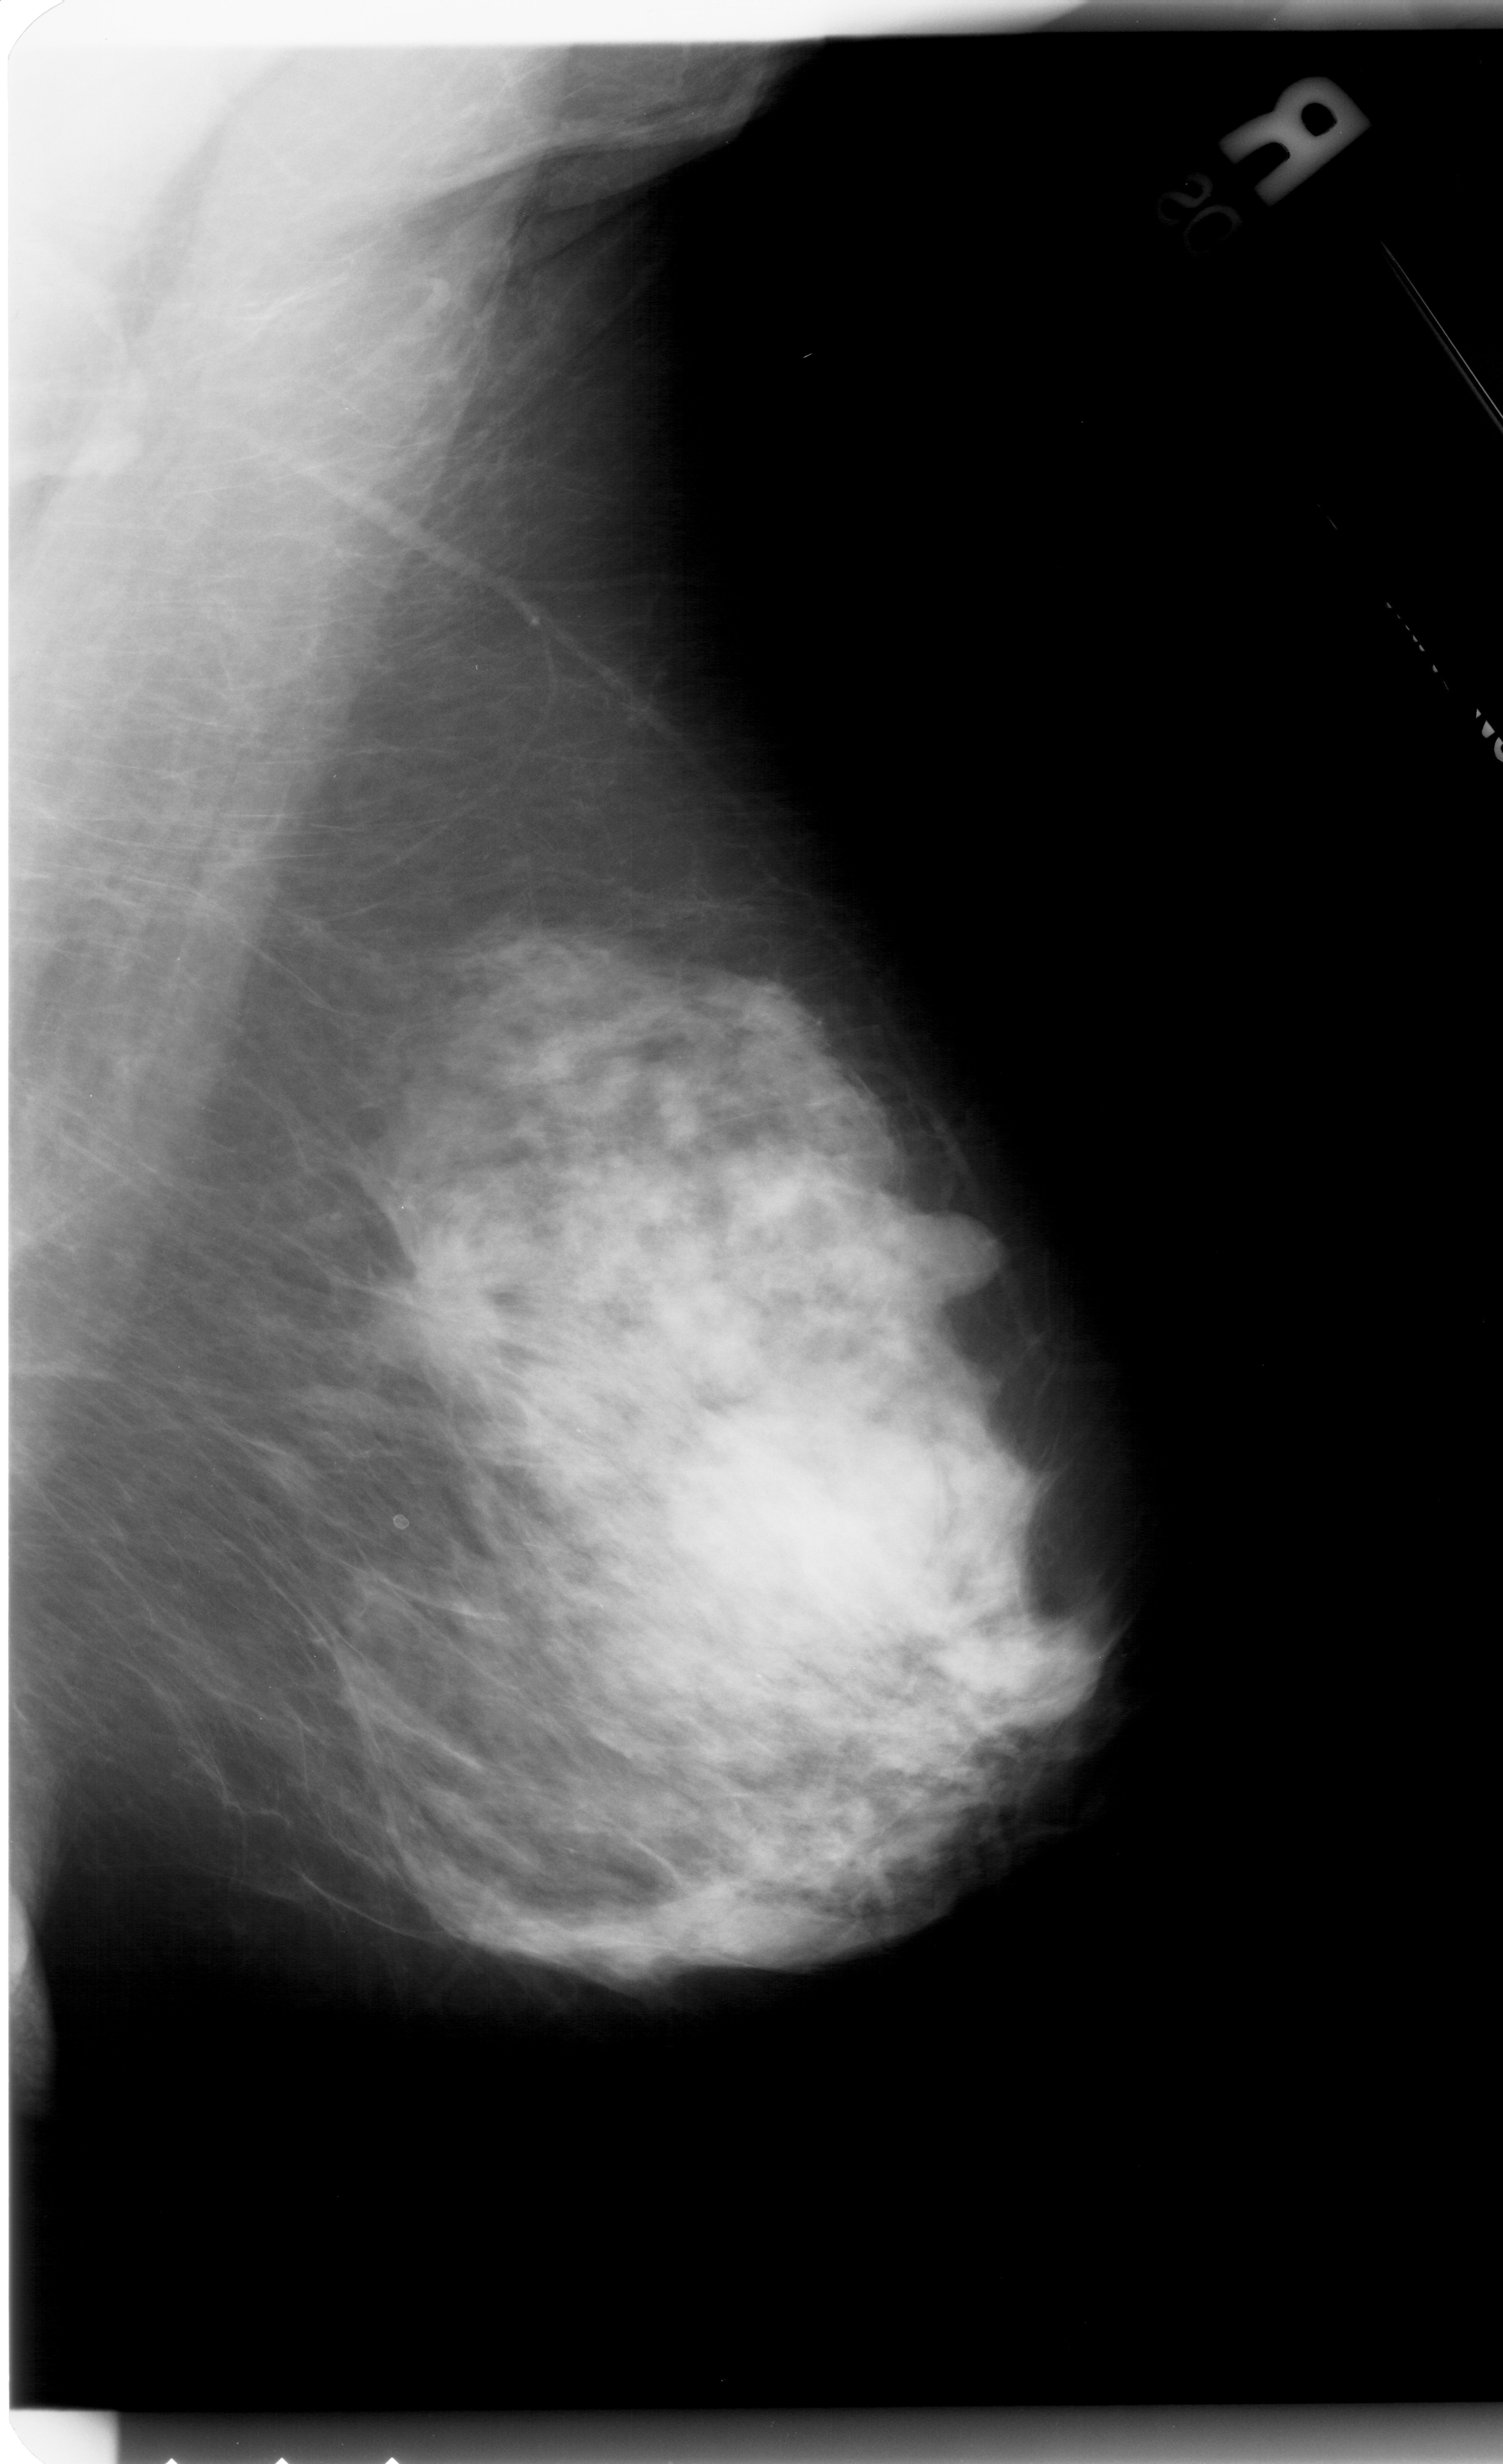
Scanned film-screen mammogram. Right breast. MLO view. Breast composition: extremely dense (BI-RADS density category 4 of 4). 1503 × 2464 image matrix.
Expert-marked regions of interest on this image (one box per marked abnormality):
- mass, shape irregular, margins spiculated; BI-RADS assessment category 5; subtlety rating 4 on a 1 (subtle) to 5 (obvious) scale; pathology (as recorded): malignant: box from (x=362, y=1231) to (x=537, y=1396) px